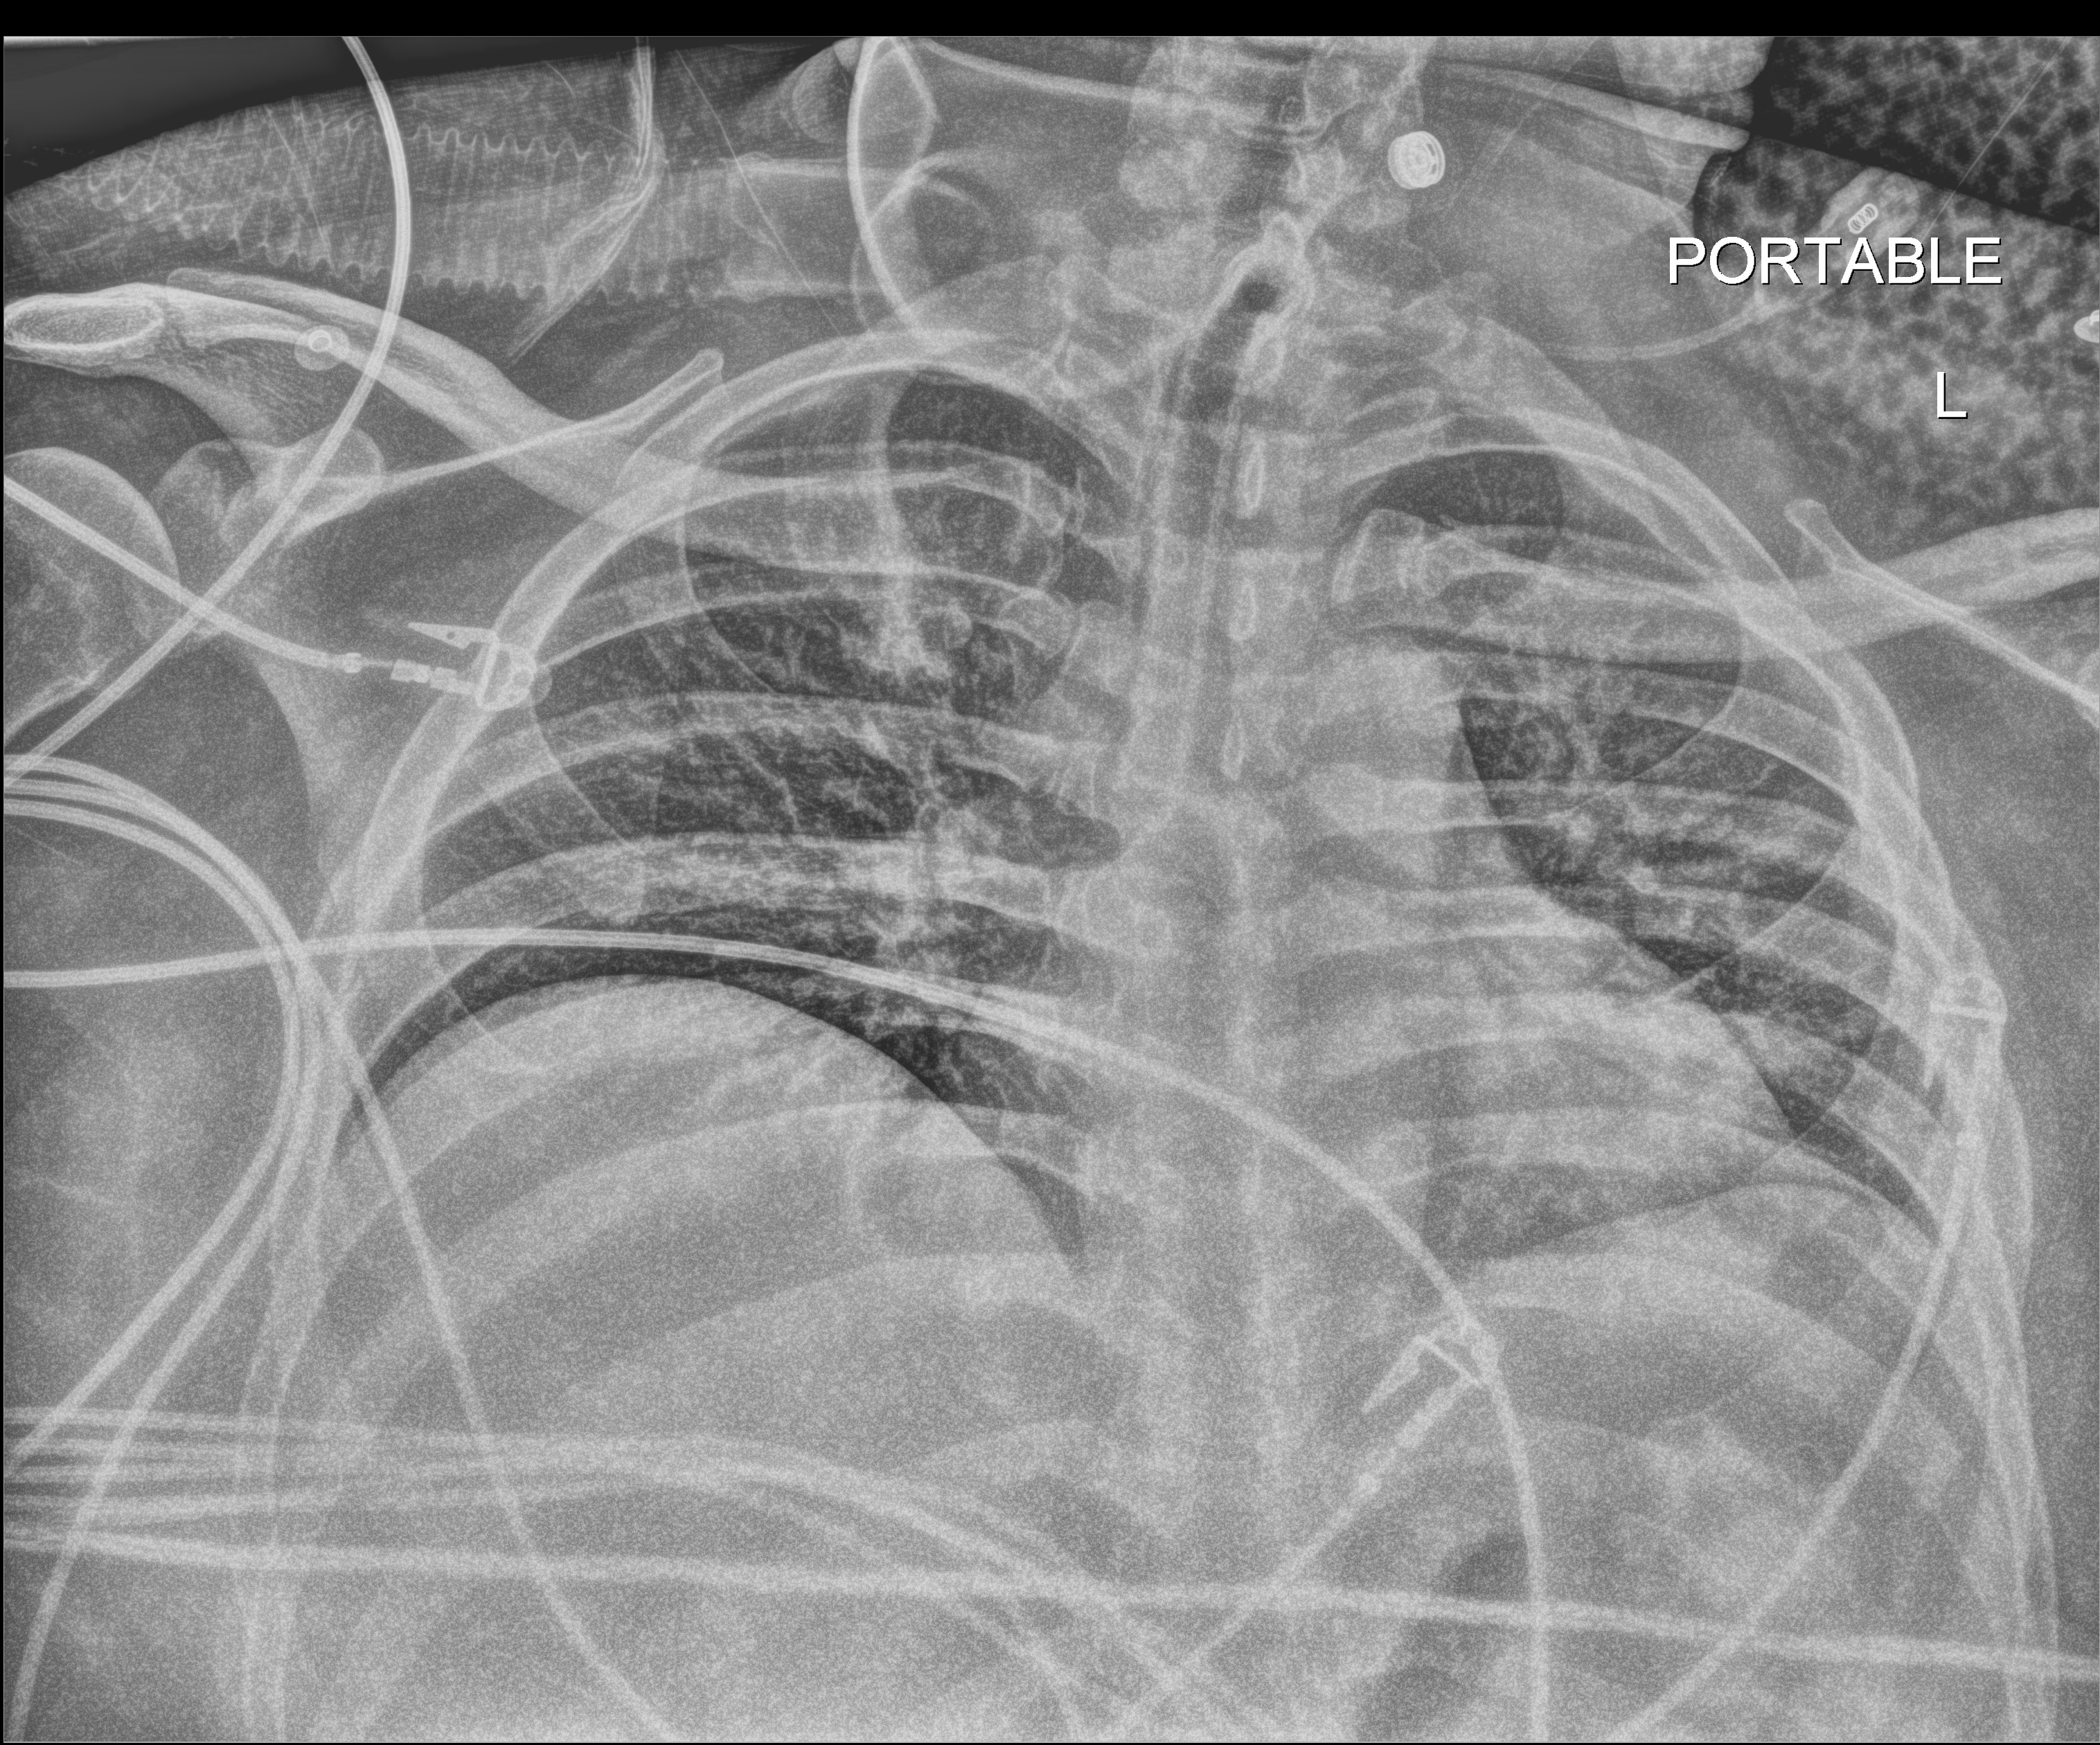
Bedside chest radiograph (digital radiography); anteroposterior (AP) projection. Patient hospitalised with COVID-19; male, aged 18–59 years.
From the hospital-stay record, not from the radiograph (when in the stay this image was taken is not recorded): other chronic lung disease (admission record): yes; mechanically ventilated during this hospital stay: yes.